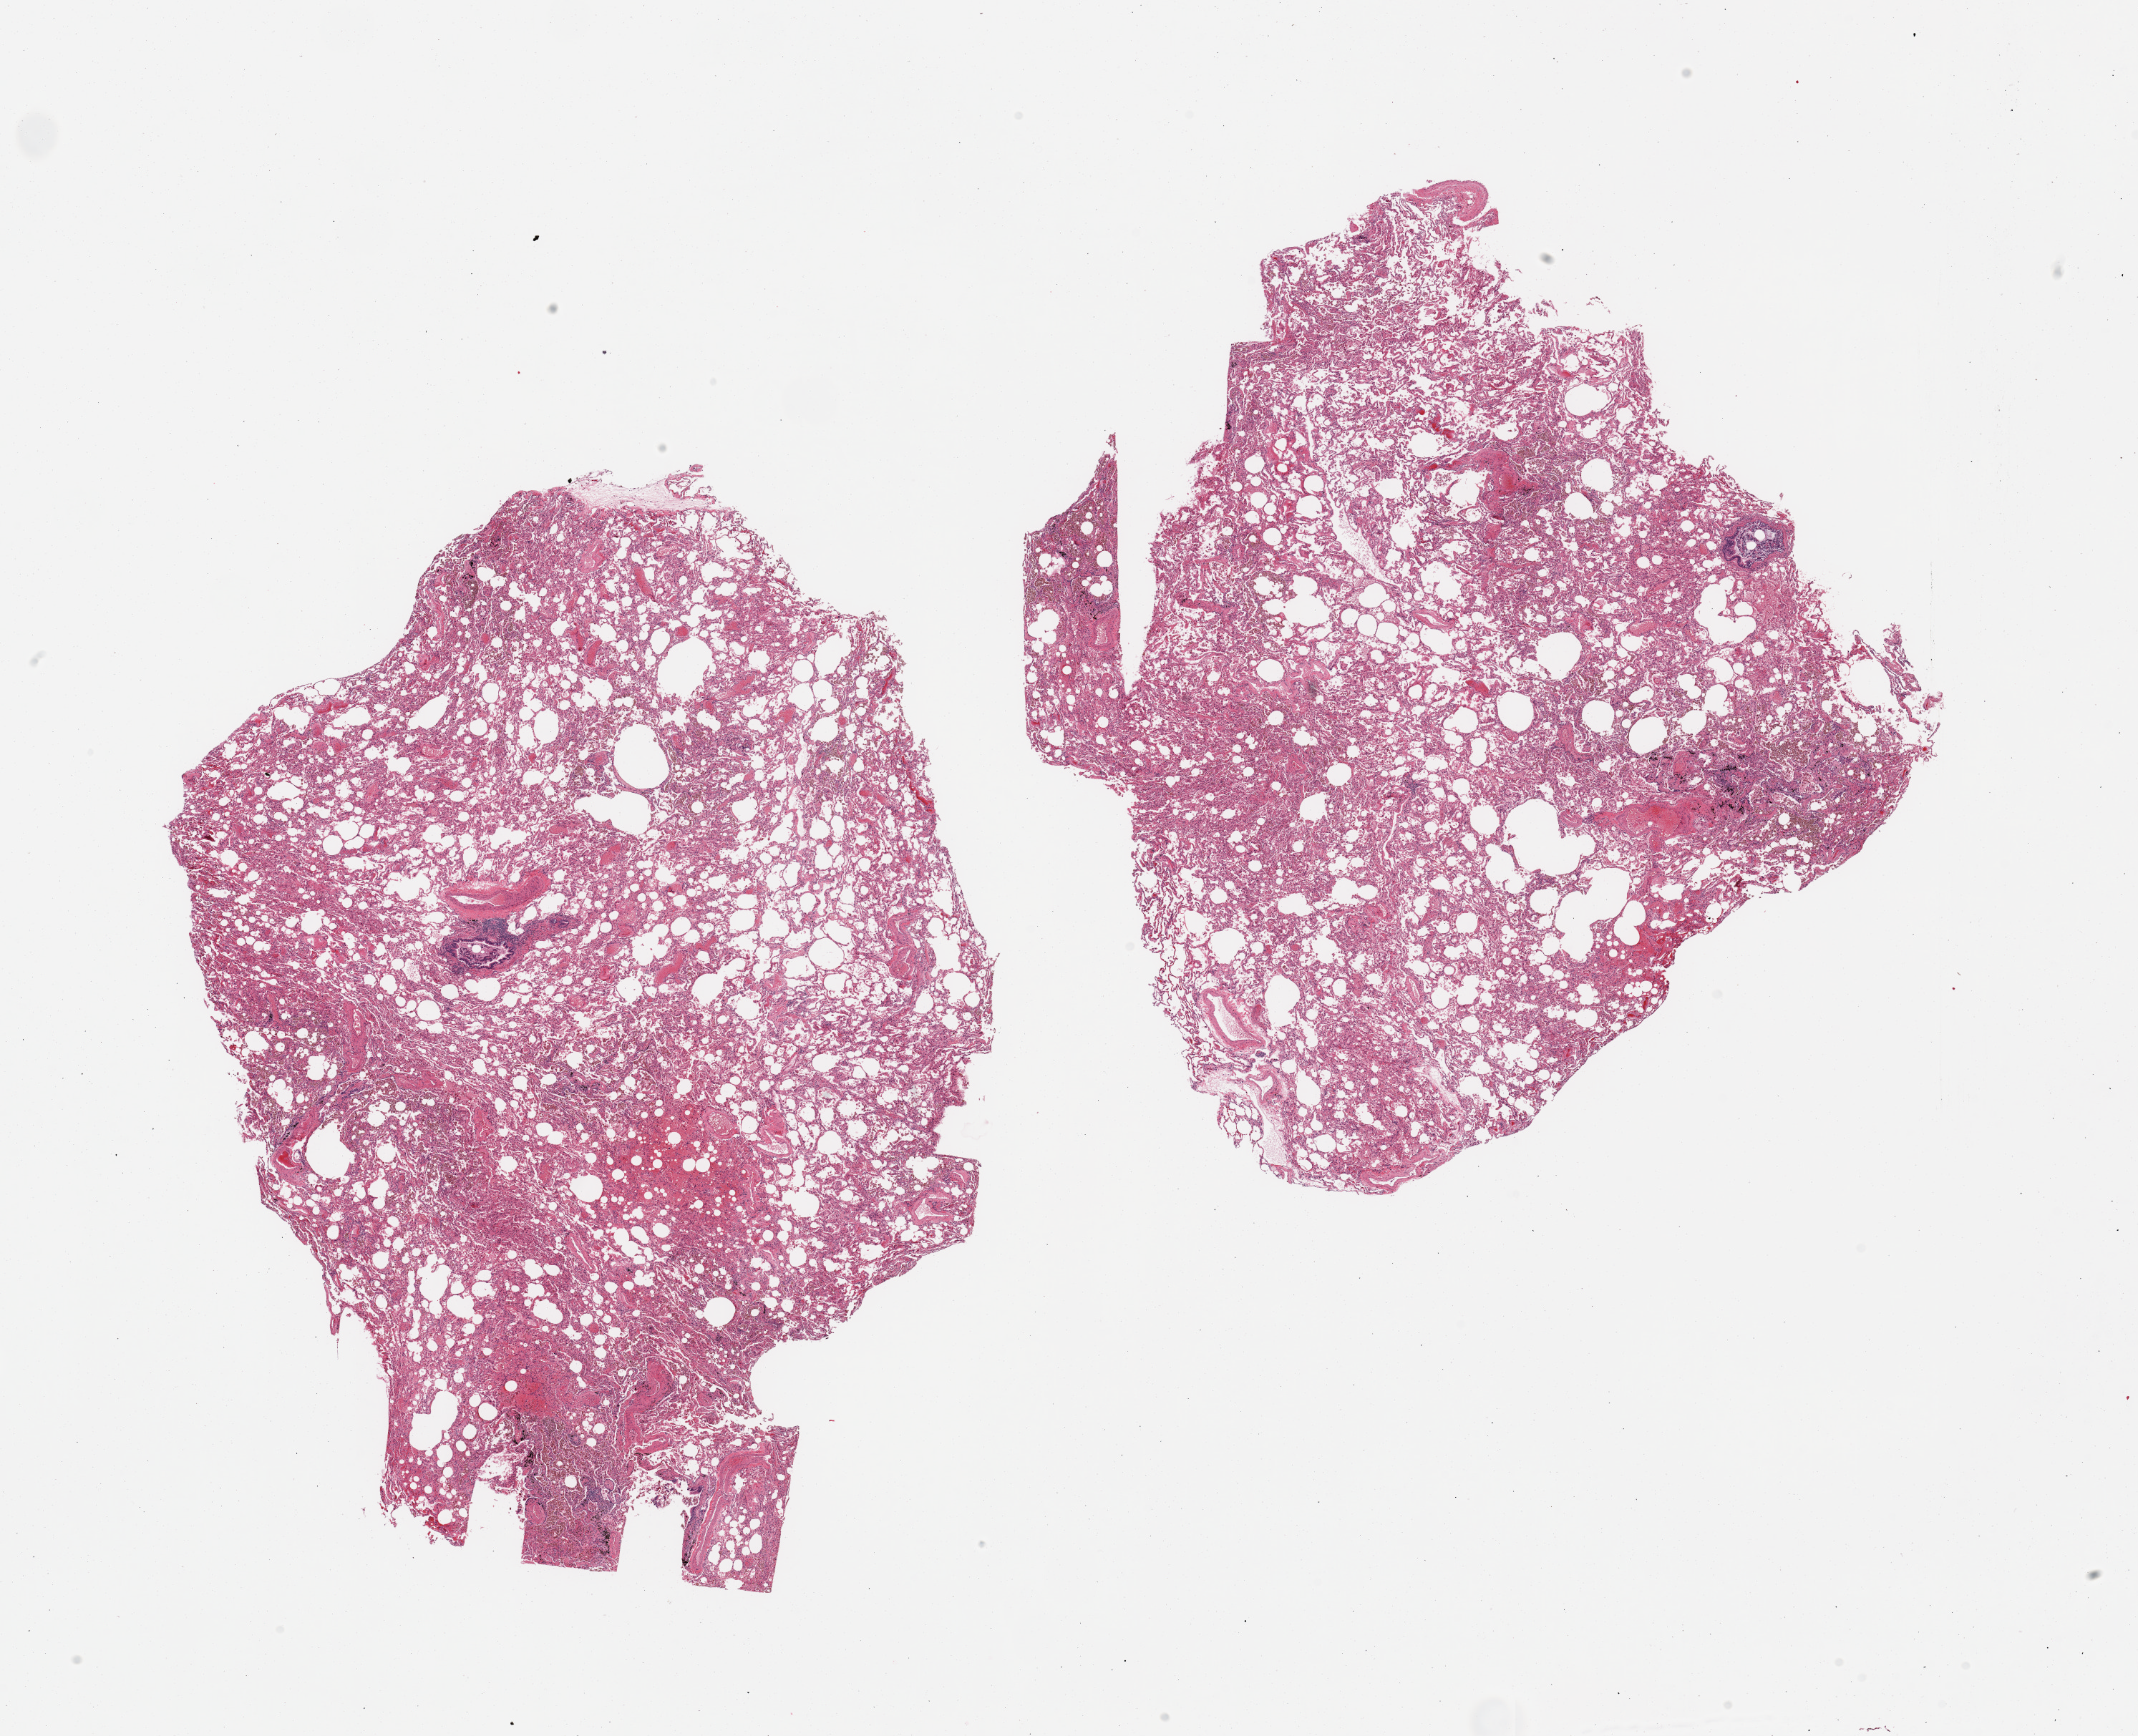
Hematoxylin and eosin (H&E) whole-slide image, low-resolution overview of the scanned area, about 23.6 x 19.2 mm; PAXgene-fixed paraffin-embedded (PFPE) section; sampled site (target tissue): lung; tissue donor sample. Donor sex: male.
• reviewer comment on this tissue sample: 2 pieces, moderate congestion